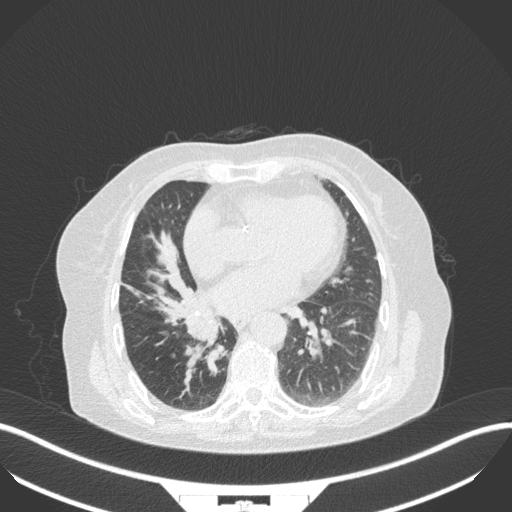
Chest CT, one axial slice. Position 131 of 329 along the scan axis. Reconstruction kernel B31f. 120 kVp. Lung window (W 1500 / L -600 HU). 1 mm slice thickness. 512 × 512 image matrix, field of view 400 × 400 mm. Female patient, age 75 years. Case-level facts recorded for this patient, not image findings: clinical TNM (as recorded): T1b N0 M1a; histopathological grade: G1.
Outlined on this slice (rectangle marked by the reading radiologist):
- lung tumour (recorded histology: squamous cell carcinoma): bounding box [x1, y1, x2, y2] px = [180, 311, 223, 379]